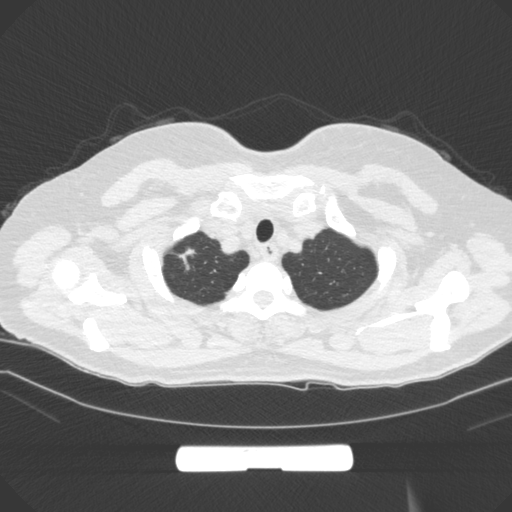
Chest CT, one axial slice. Slice 265 of 295 in the series (ordered by position). Lung window (W 1500 / L -600 HU). 1 mm slice thickness. 512 × 512 image matrix. Patient: female, 58 years. From the clinical record (not read from this slice): clinical TNM (as recorded): T1b N0 M0; histopathological grade: G2-3.
Annotated regions visible in this slice (bounding box drawn by a radiologist):
- lung tumour (recorded histology: adenocarcinoma): box from (x=171, y=244) to (x=202, y=284) px